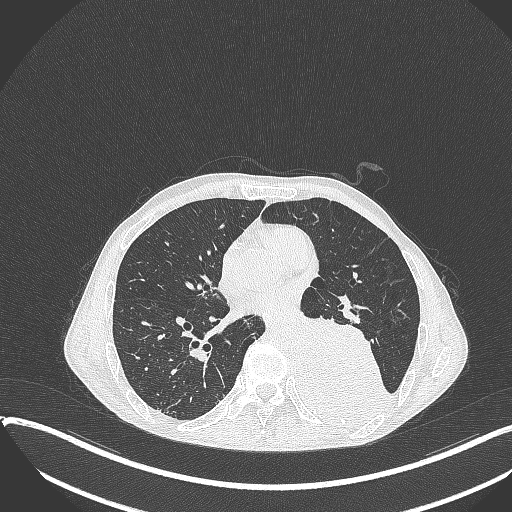
Chest CT, one axial slice. Slice 168 of 401 in the series (ordered by position). Reconstruction kernel B70f. Lung window (W 1500 / L -600 HU). 1 mm slice thickness. 512 × 512 image matrix, field of view 400 × 400 mm. Patient: male, 57 years. Case-level facts recorded for this patient, not image findings: clinical TNM (as recorded): T4 N0 M0.
Structures marked on this image (bounding box drawn by a radiologist):
- lung tumour (recorded histology: squamous cell carcinoma): bounding box (x1, y1, x2, y2) in pixels: (291, 308, 393, 427)